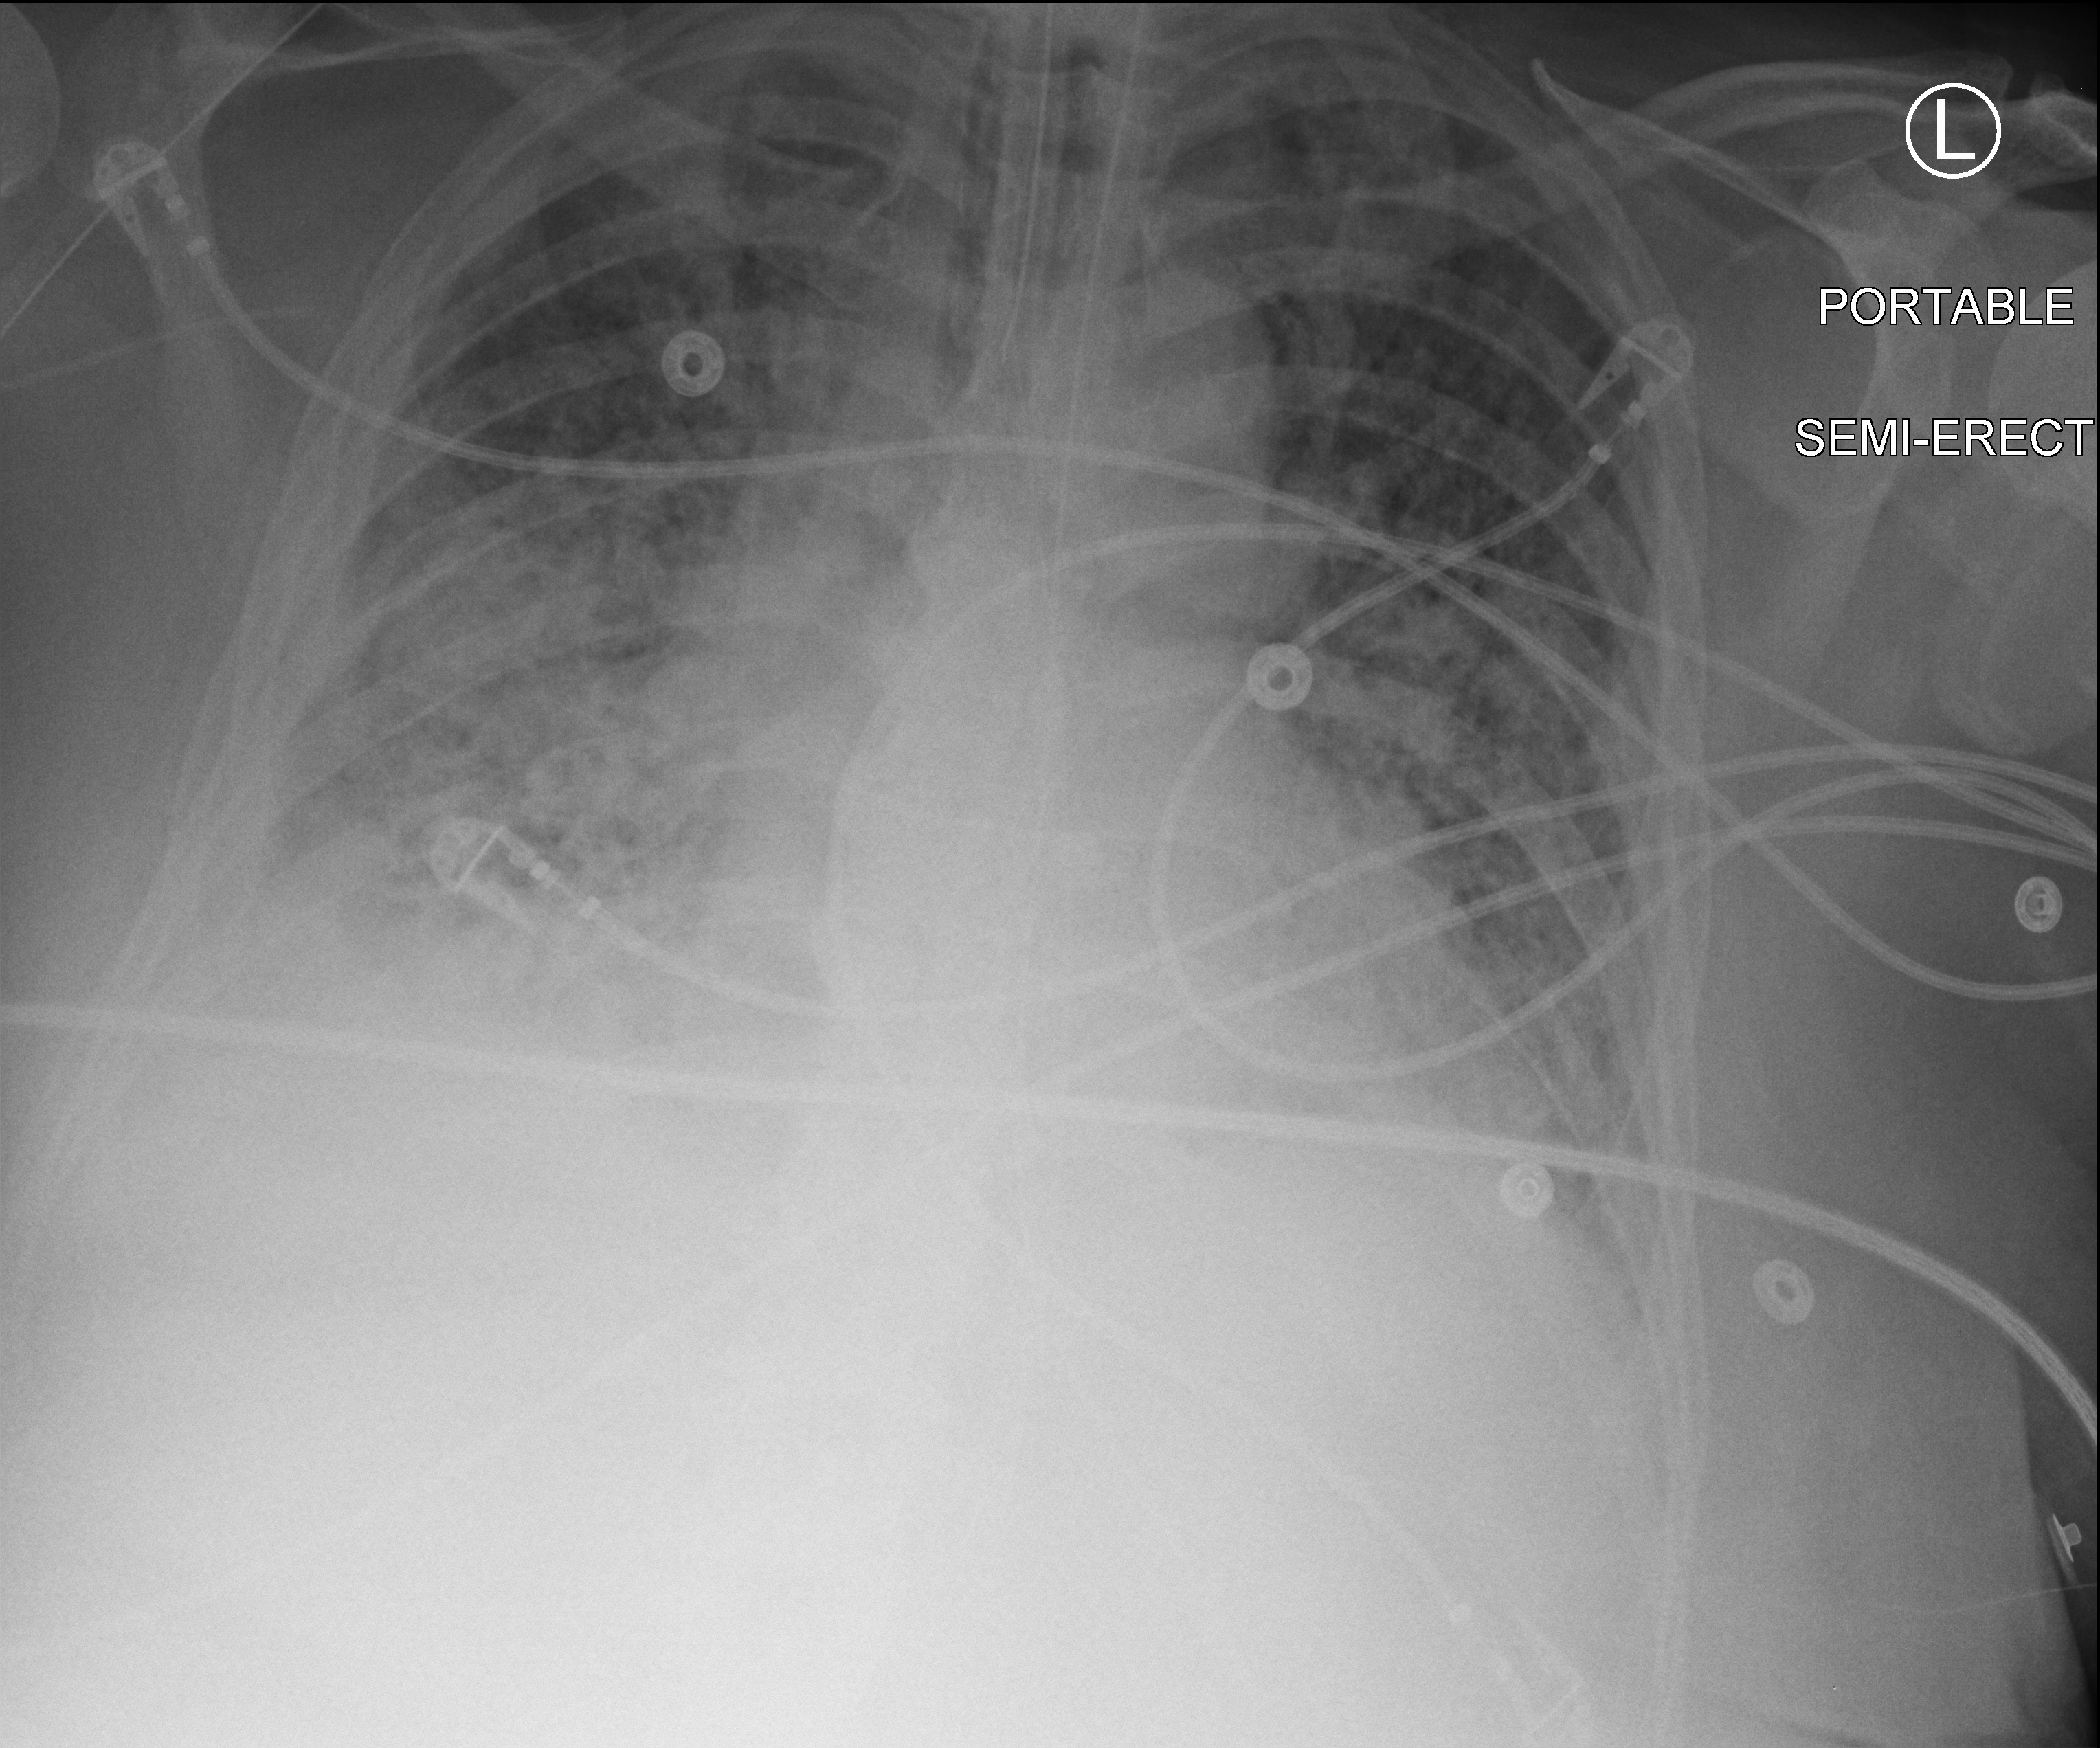
Chest X-ray (portable); anteroposterior (AP) projection. Patient hospitalised with COVID-19; male, aged 60–74 years.
Admission-level facts for this patient (not findings on this image; timing relative to this image not recorded): diabetes (admission record): no.